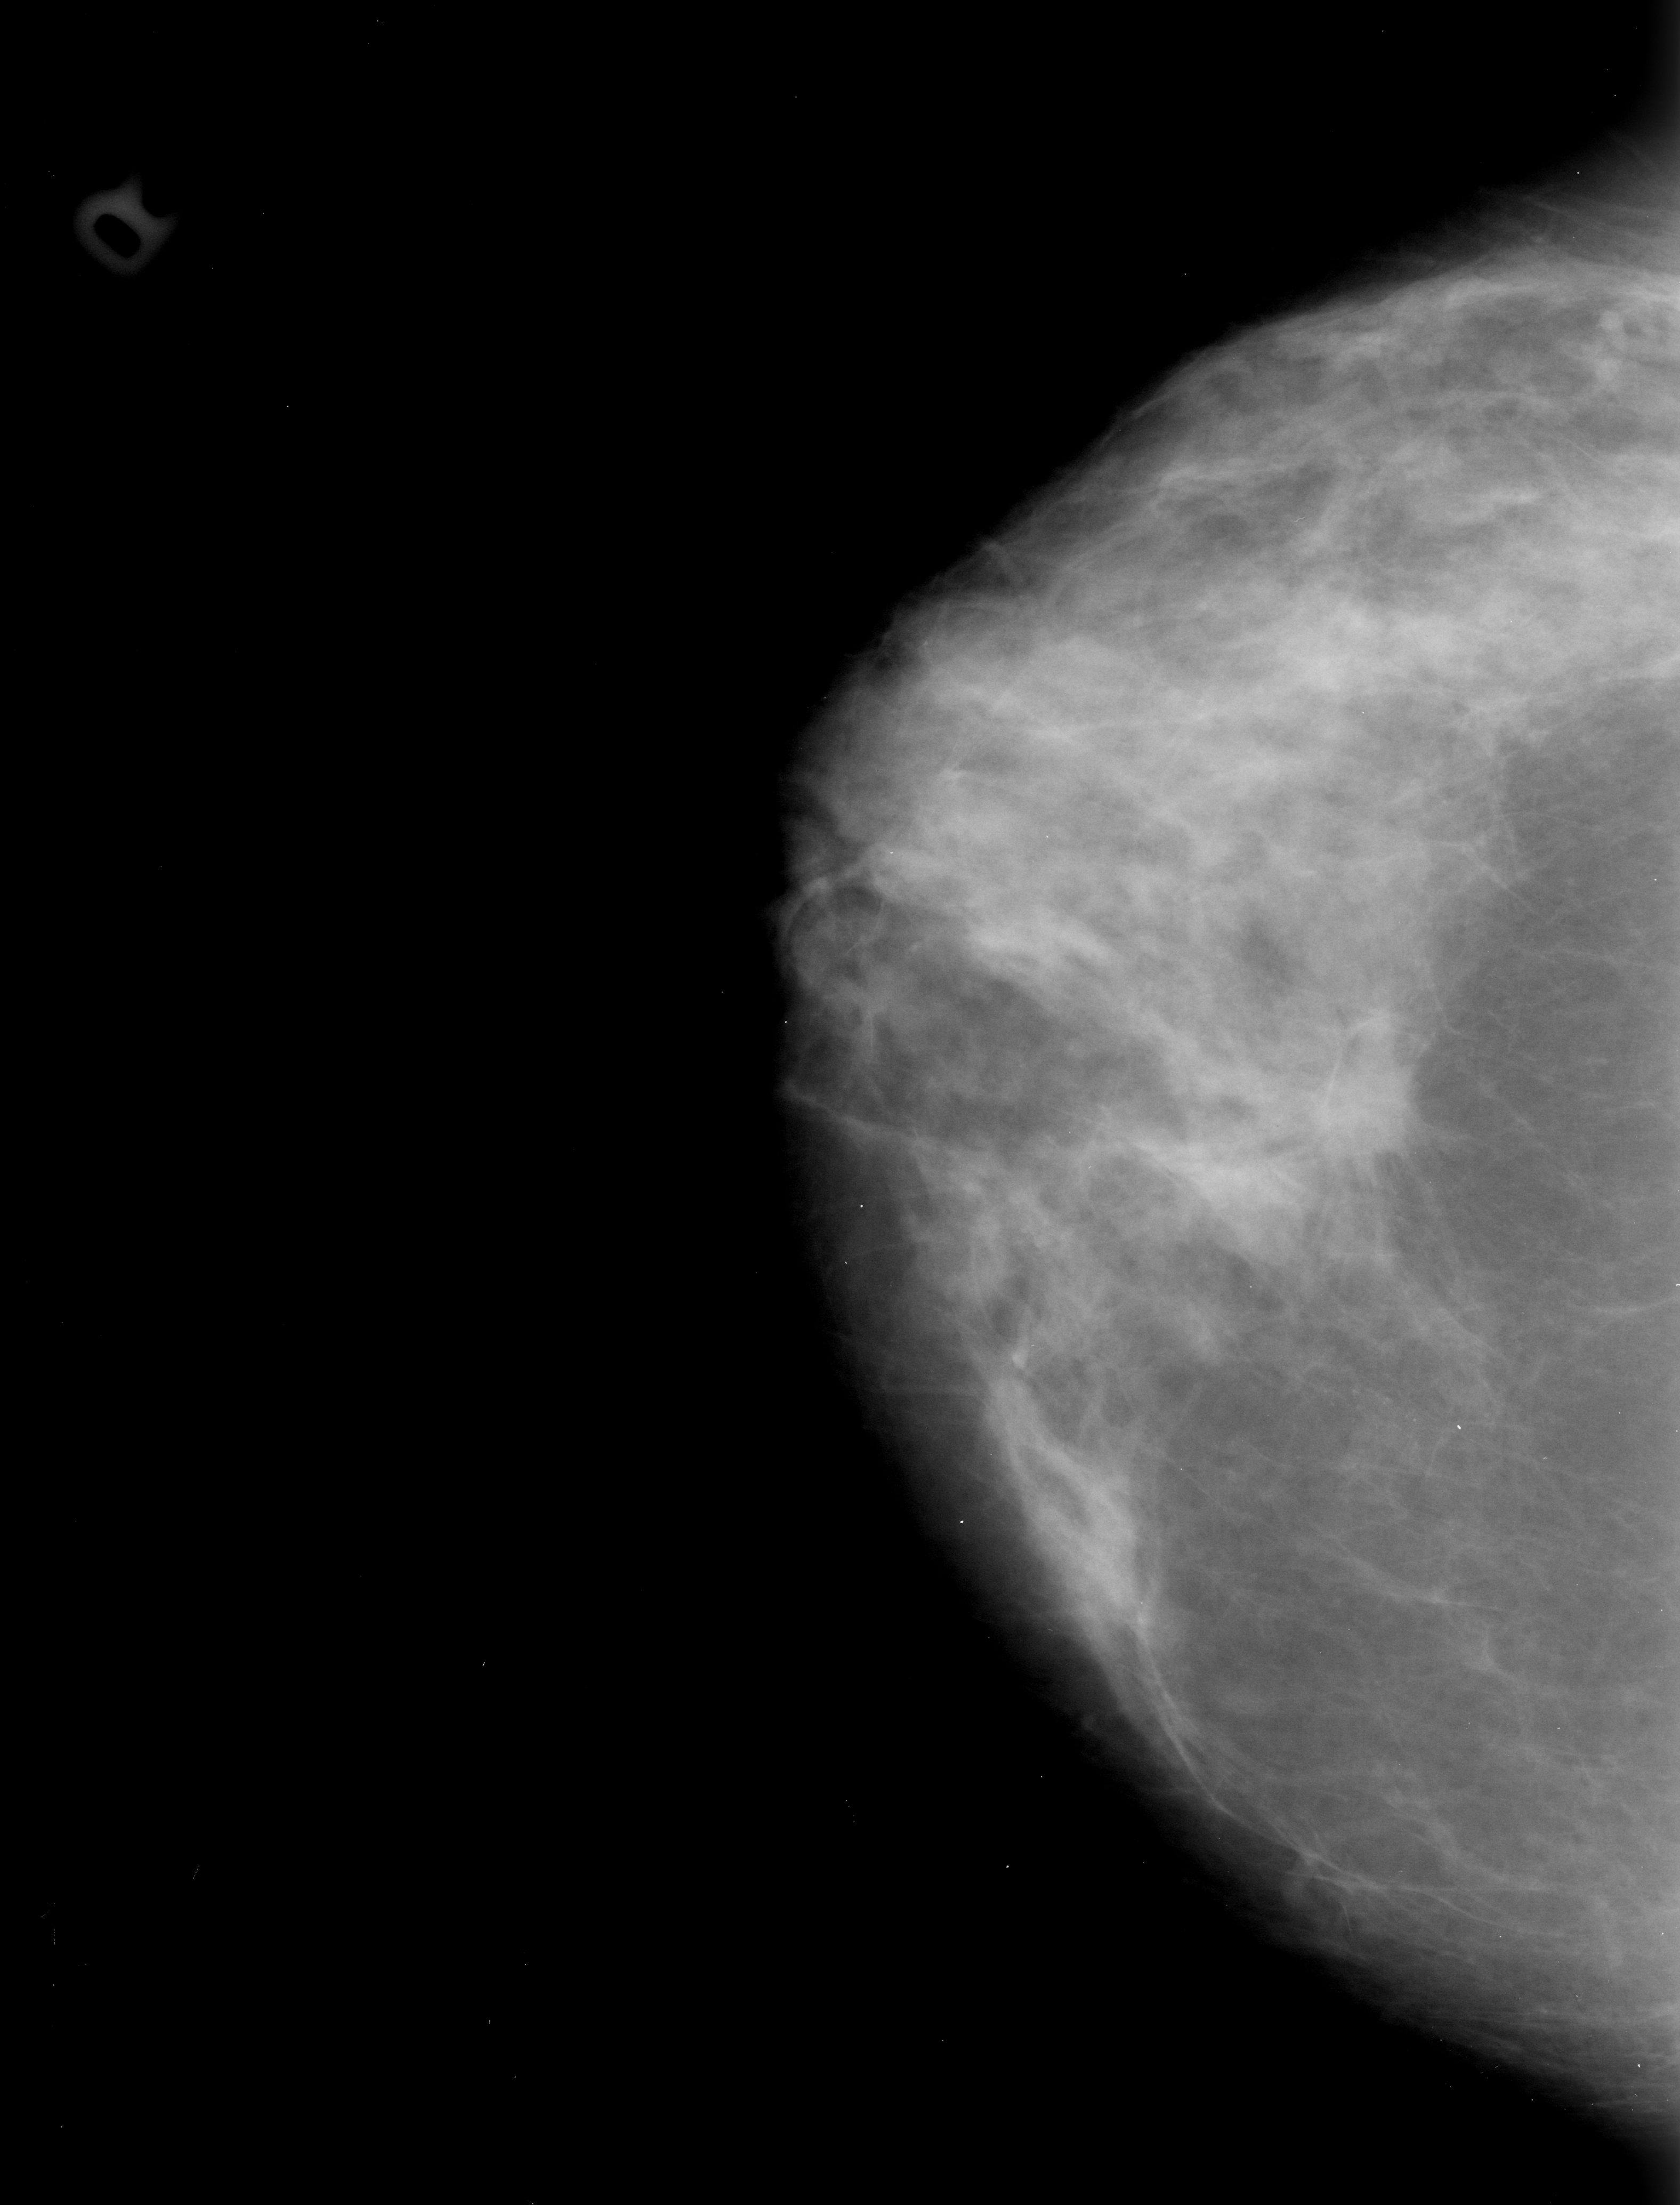
Digitized screen-film mammogram; right breast; craniocaudal (CC) view; breast composition: heterogeneously dense (BI-RADS density category 3 of 4).
Finding: mass, shape irregular / architectural distortion, margins spiculated; BI-RADS assessment category 4; subtlety rating 3 on a 1 (subtle) to 5 (obvious) scale; pathology (as recorded): malignant.